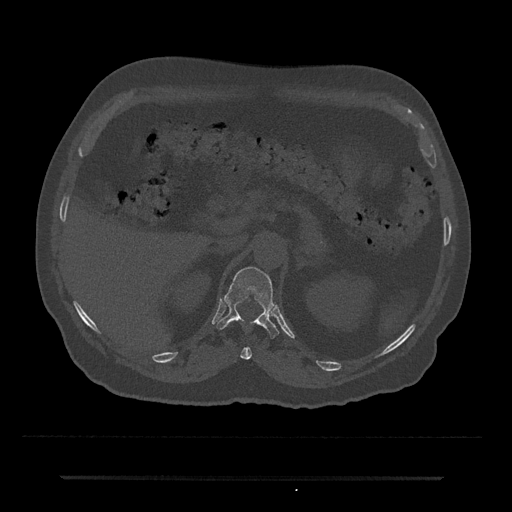
CT including the spine, one axial slice; slice 139 of 797 in the series (ordered by position); reconstruction kernel Br40s/3; bone window (W 1800 / L 400 HU); 0.5 mm slice thickness; 512 × 512 image matrix. Male patient, age 69 years. Case-level facts recorded for this patient, not image findings: primary cancer: prostate.
Annotated regions visible in this slice (semi-automatic segmentation, software-assisted and operator-edited):
- T11 vertebra: bounding box (x1, y1, x2, y2) in pixels: (232, 320, 252, 360)
- T12 vertebra: (216, 267, 279, 338)